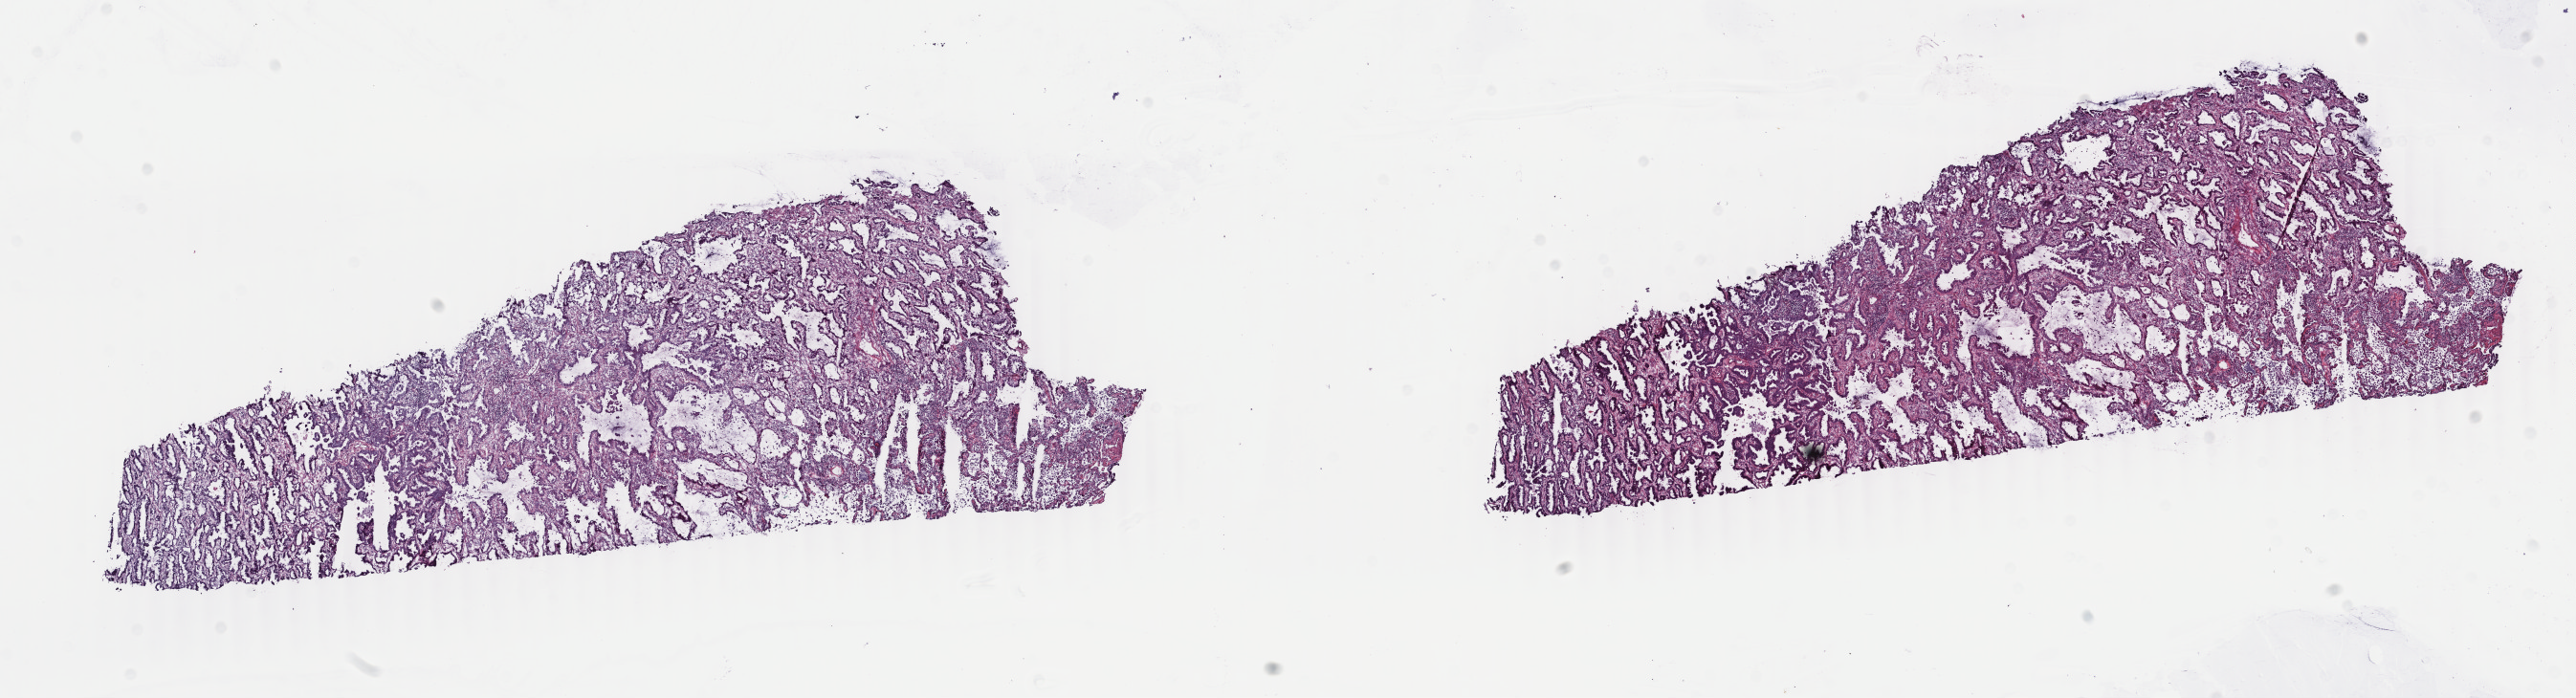
Whole-slide histology image, H&E — low-resolution overview of the scanned area, about 21.4 x 5.8 mm; frozen section from the top of the tissue portion; primary tumour sample from the lung. Female, age 76 years at initial diagnosis.
Diagnosis: Adenocarcinoma, NOS (lower lobe, lung).